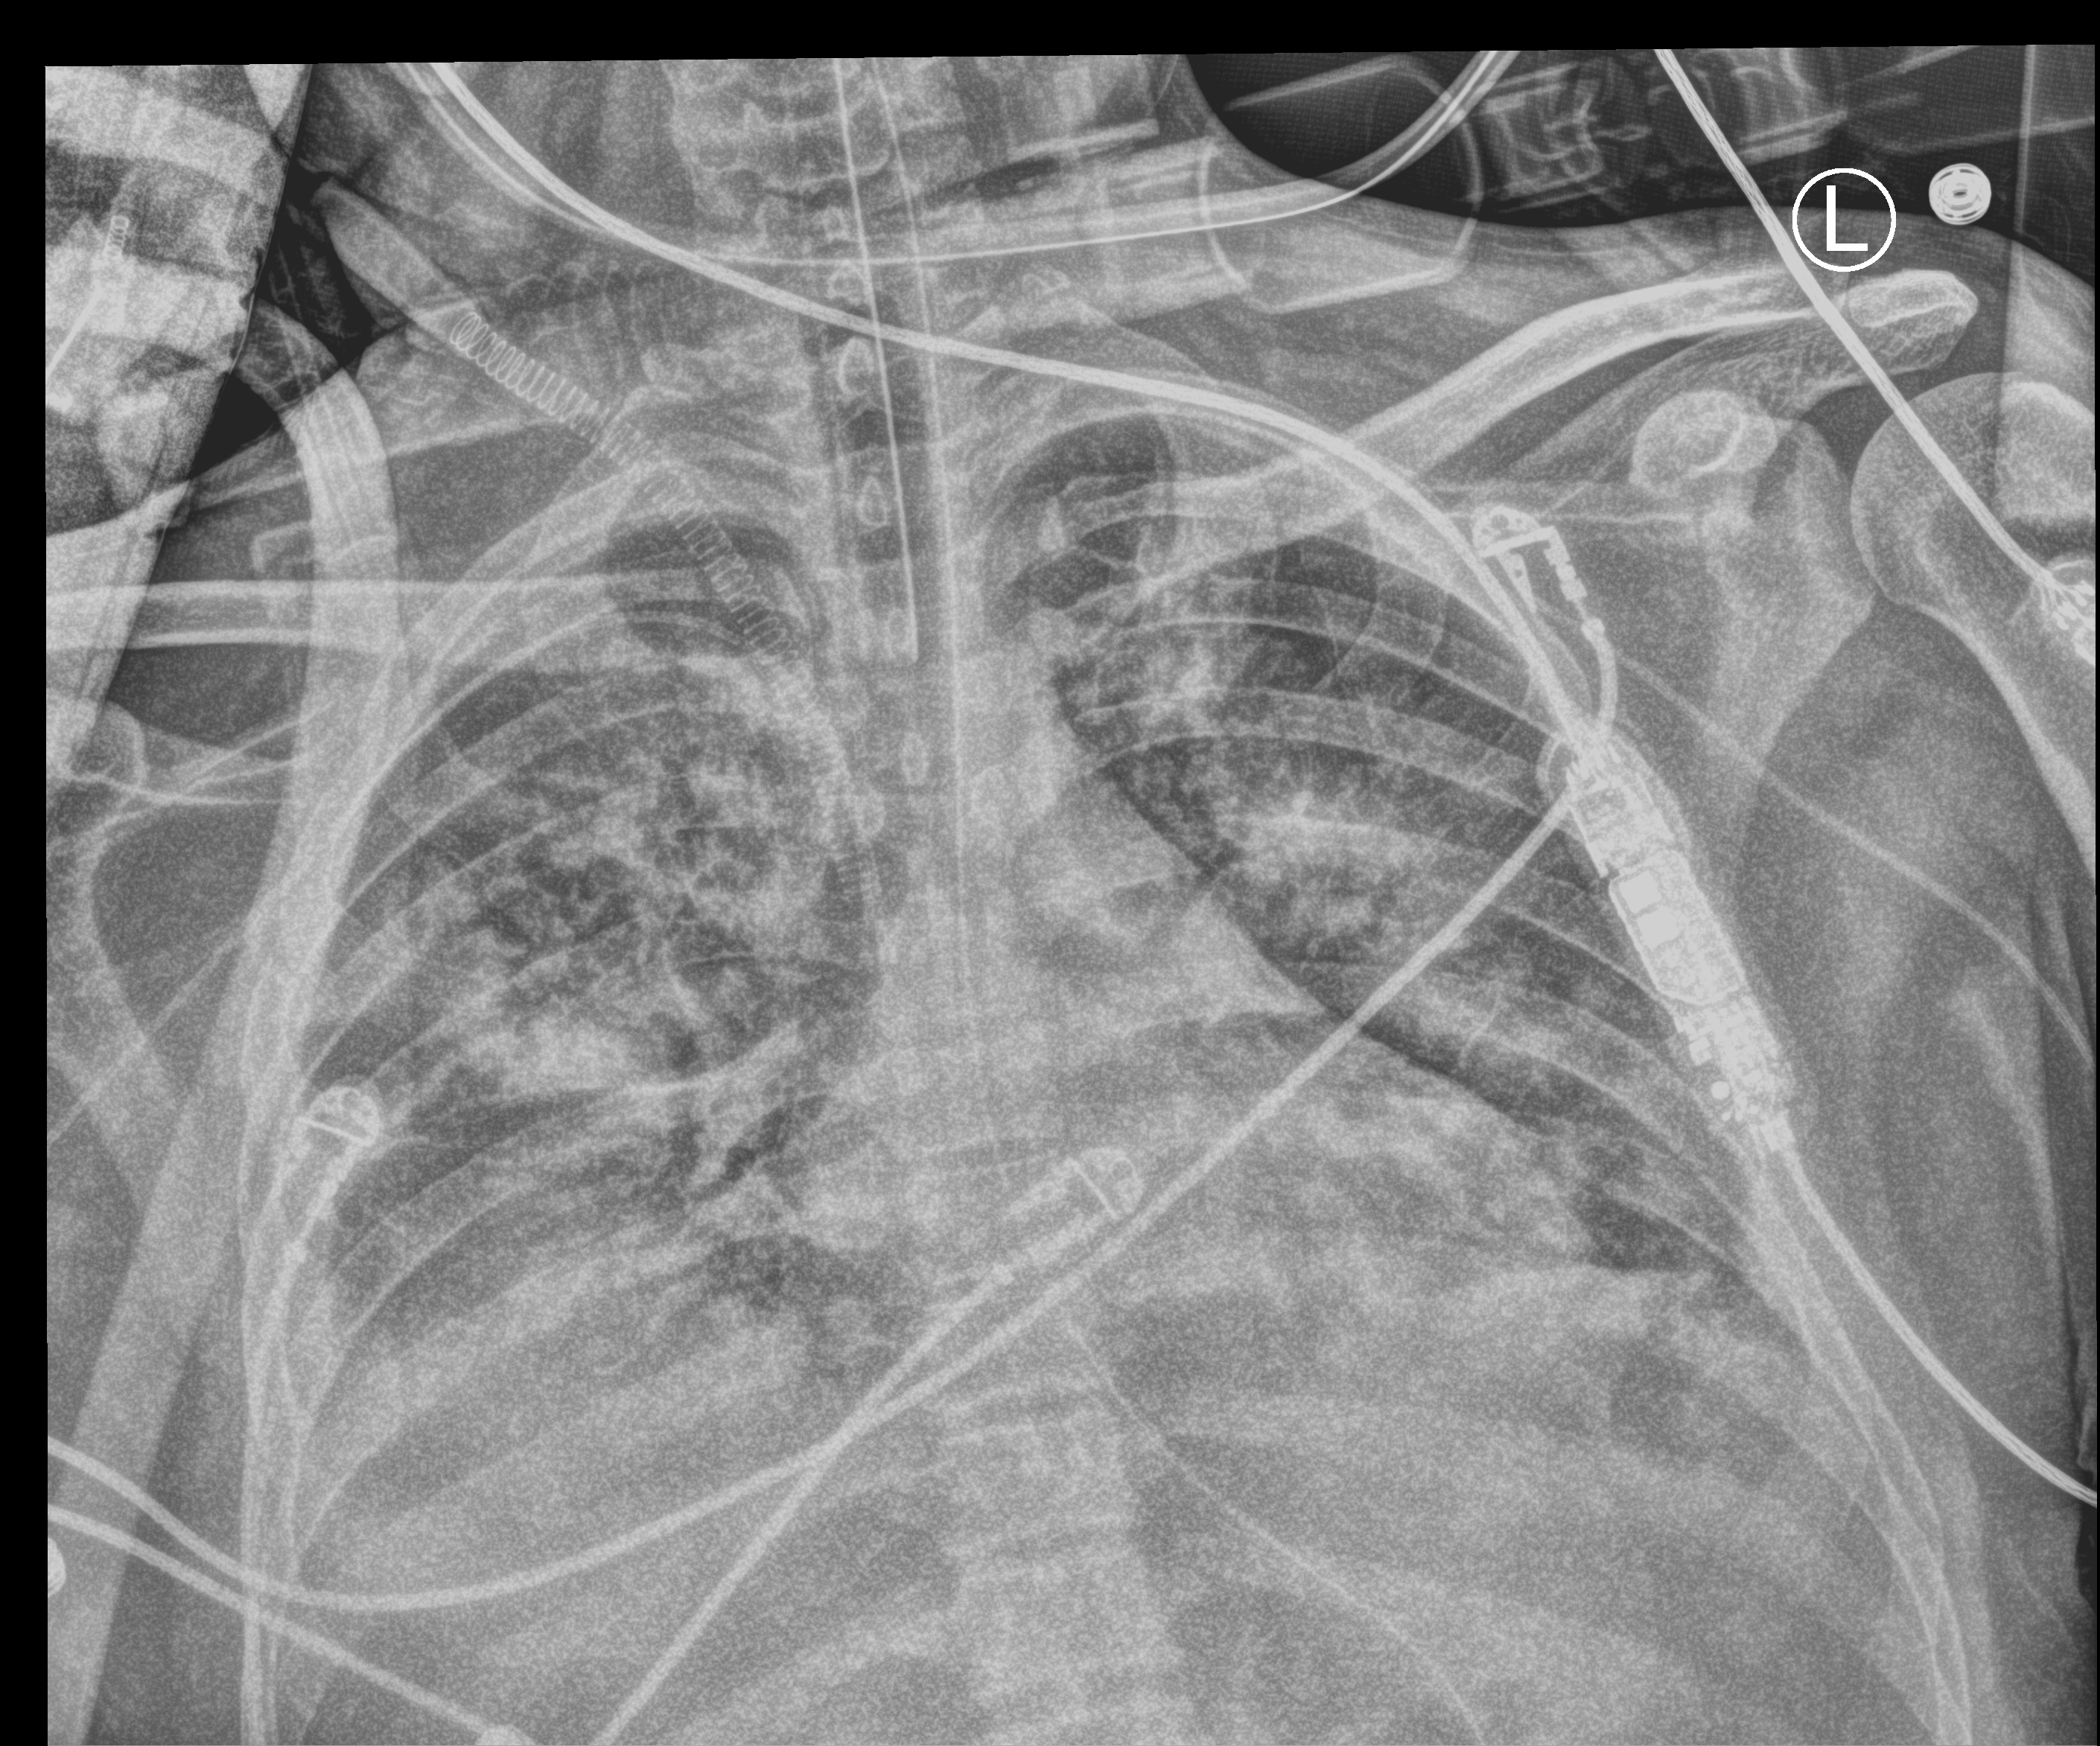
Chest X-ray (portable); anteroposterior (AP) projection. Patient hospitalised with COVID-19, aged 18–59 years.
From the hospital-stay record, not from the radiograph (when in the stay this image was taken is not recorded):
- hypertension (admission record): no